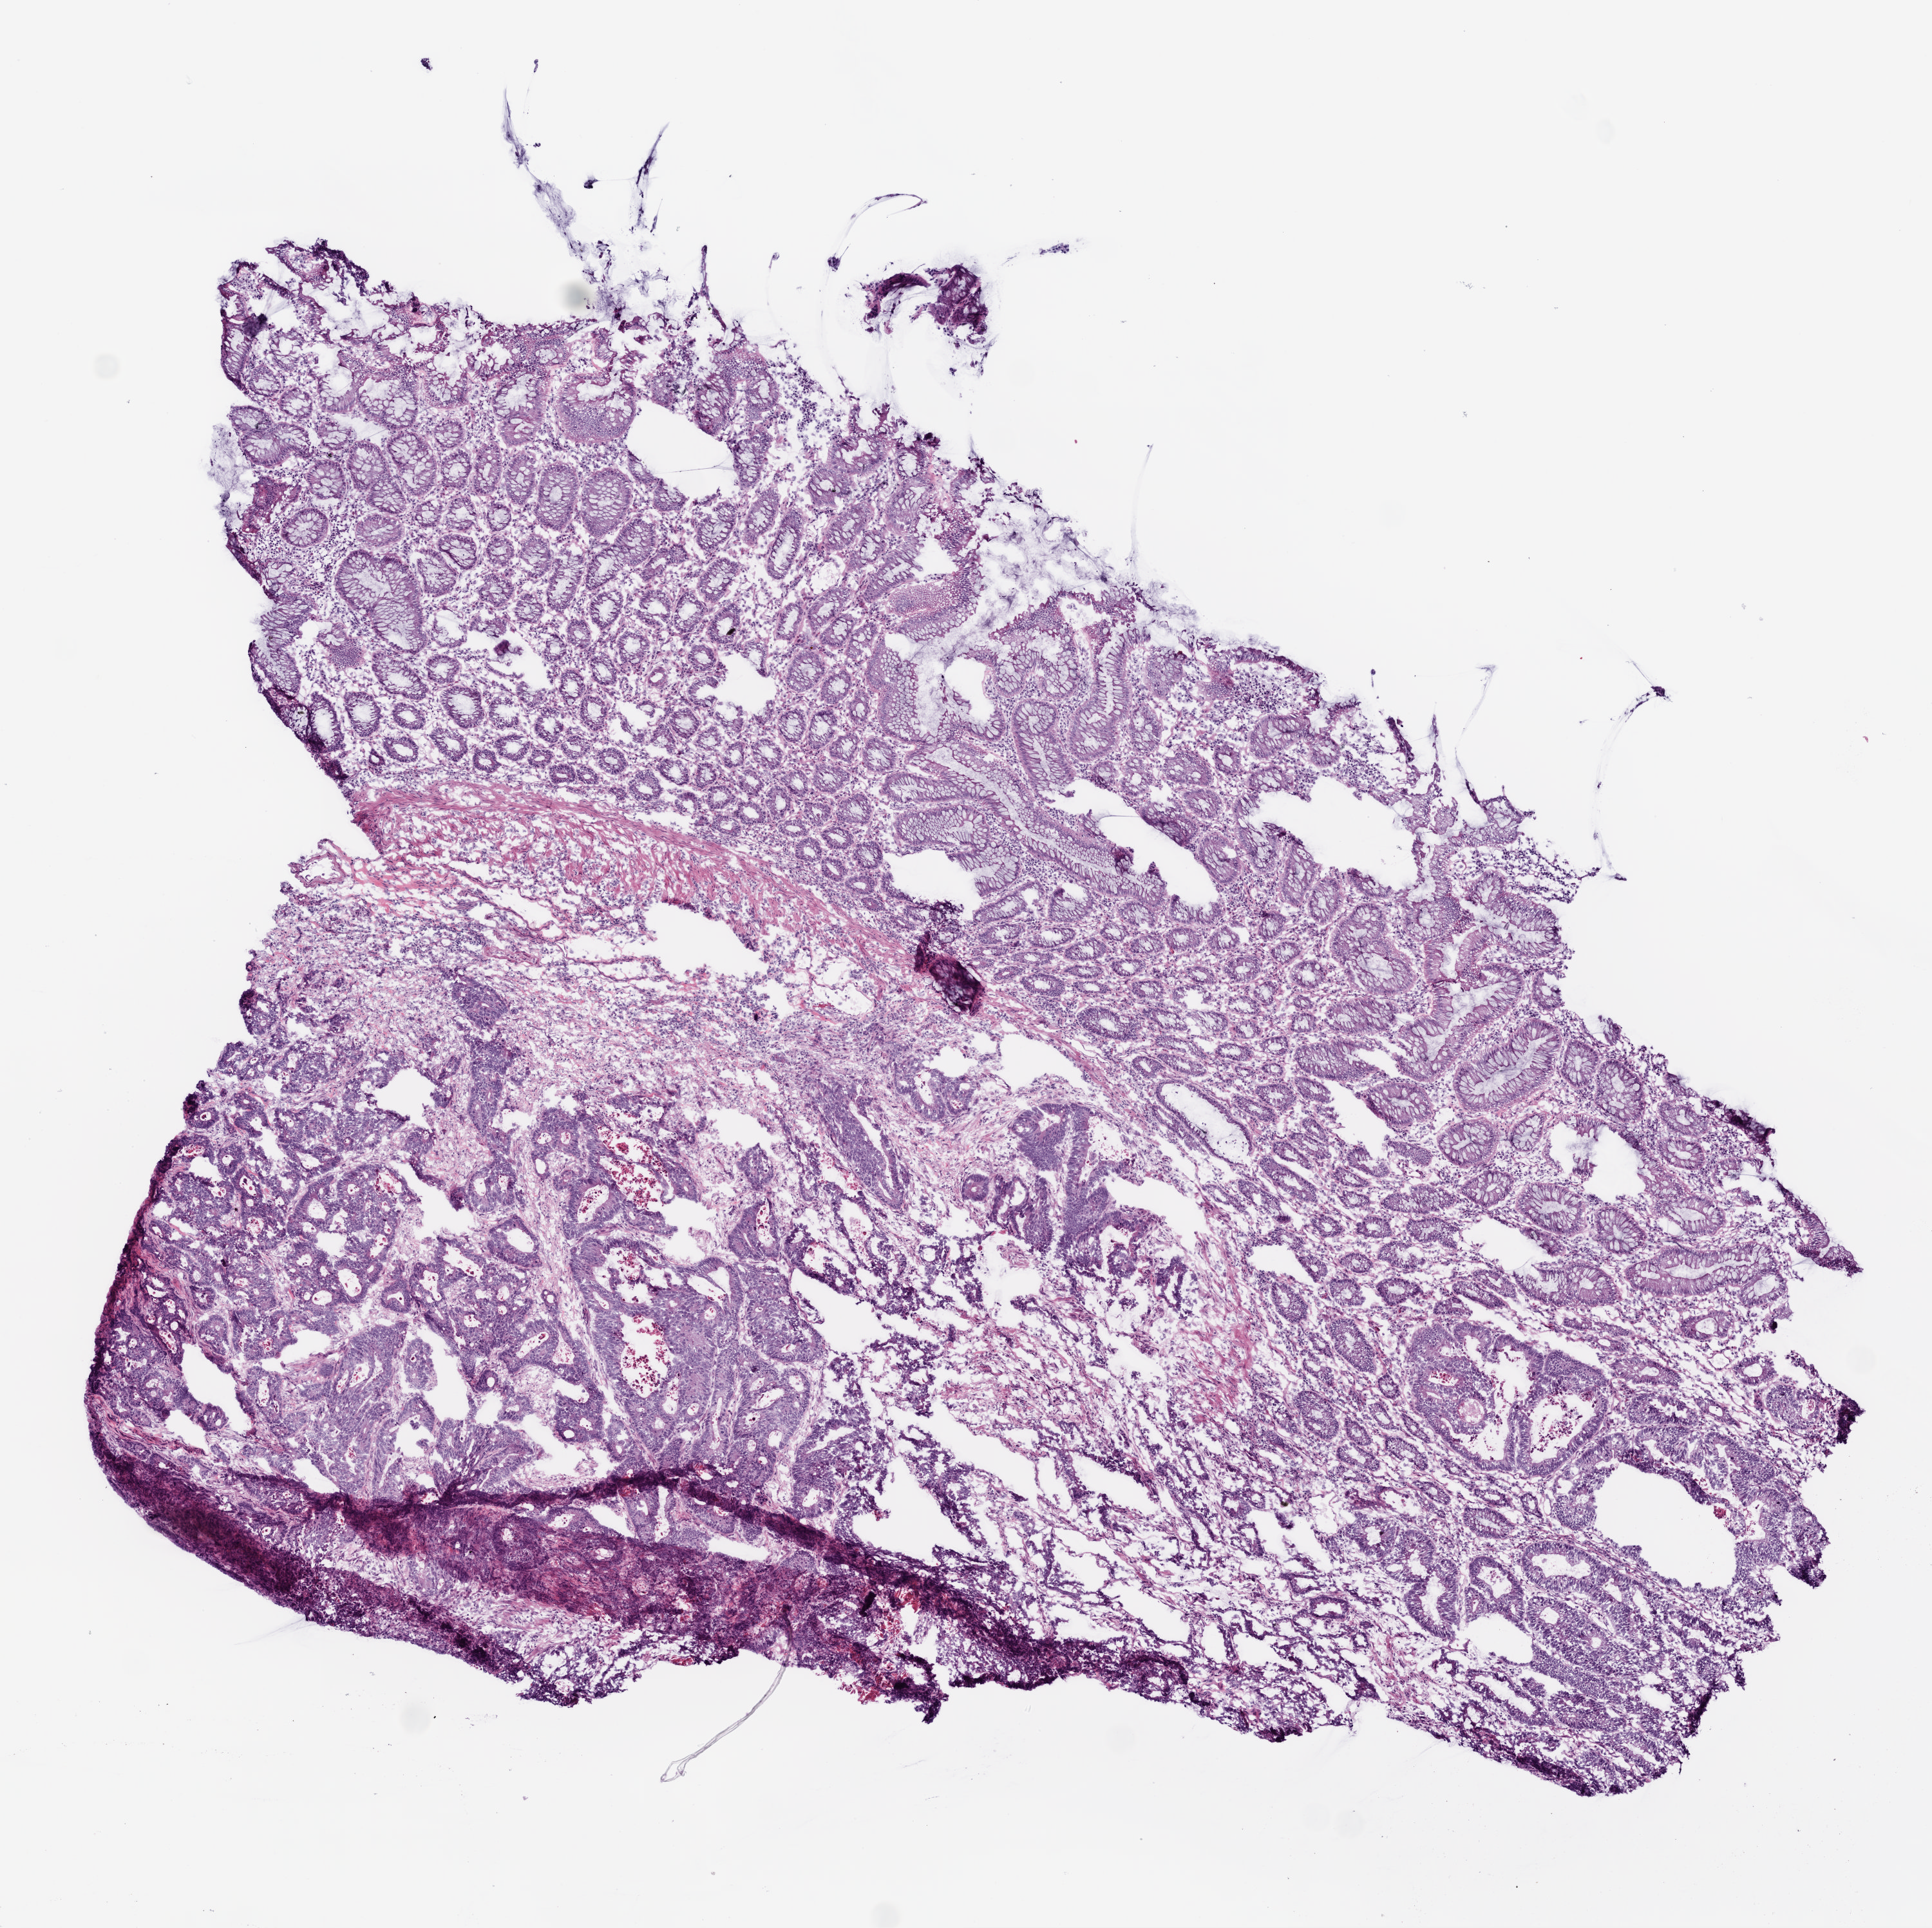
Whole-slide histology image, Hematoxylin and eosin (H&E) stained — low-resolution overview of the scanned area, about 6.0 x 6.0 mm (from a 20x scan). Frozen section from the top of the tissue portion. Rectum, primary tumour sample. Female, age 84 years at initial diagnosis. Slide review estimates, as recorded: tumour cells 47%, tumour nuclei 65%, normal cells 40%, stromal cells 5%, necrosis 8%.
AJCC pathologic stage: I. Diagnosis: Adenocarcinoma, NOS. TNM: T2 N0 M0.